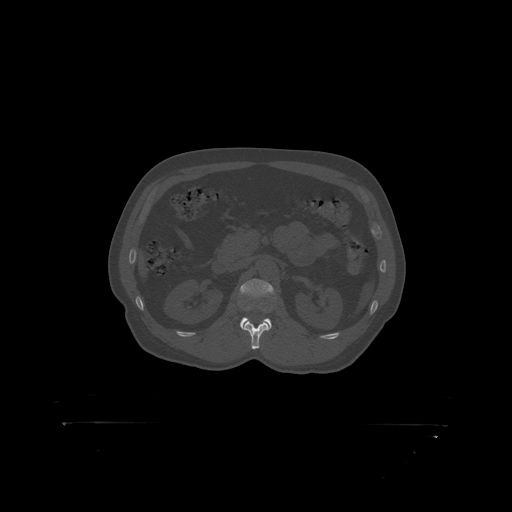
CT including the spine, one axial slice; slice 312 of 399 in the series (ordered by position); reconstruction kernel STANDARD; 120 kVp; bone window (W 1800 / L 400 HU); 1.25 mm slice thickness; 512 × 512 image matrix. Patient: male, 46 years. Case-level facts recorded for this patient, not image findings: primary cancer: skin.
Outlined on this slice (semi-automatically segmented with operator editing):
- L2 vertebra: box from (x=240, y=279) to (x=276, y=311) px